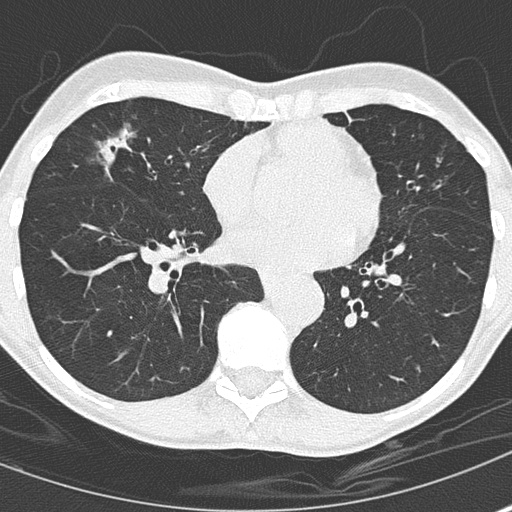
Axial slice from a low-dose chest CT screening exam, second annual screen, lung window (W 1500 / L -600 HU), 2 mm slice thickness, slice 103 of 167 in the series, 512 × 512 image matrix. Female, age 67 years at enrolment. Current smoker at enrolment.
Expert reader's lesion annotation, bounding box [x1, y1, x2, y2] px = [83, 113, 186, 203]. The screening reader recorded 2 non-calcified nodules or masses ≥4 mm on this exam (right middle lobe, right middle lobe); which of them this box marks is not recorded.